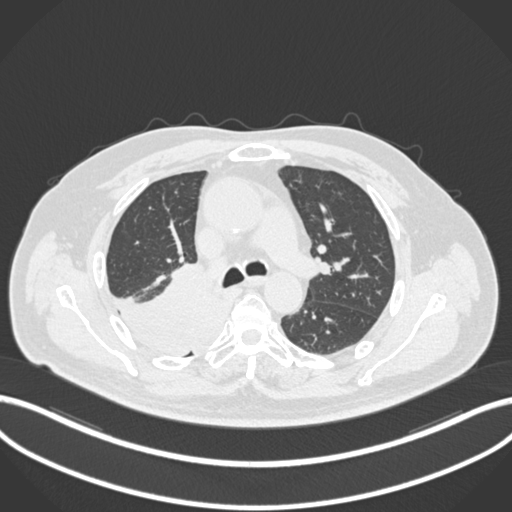
Chest CT, one axial slice. Reconstruction kernel B30f. Lung window (W 1500 / L -600 HU). 1 mm slice thickness. 512 × 512 image matrix, field of view 400 × 400 mm. Male patient, age 68 years. Case-level facts recorded for this patient, not image findings: clinical TNM (as recorded): T2a N0 M0.
Structures marked on this image (bounding box drawn by a radiologist):
- lung tumour (recorded histology: adenocarcinoma): bounding box <115,266,232,360> (left, top, right, bottom; pixels)